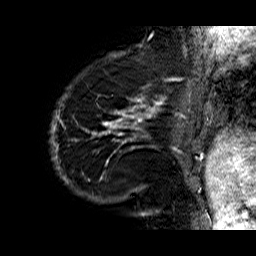
Breast MRI (dynamic contrast-enhanced), one sagittal slice. Slice 7 of 60 in the series (ordered by position). Dynamic contrast-enhanced series, time point 2 of 6 at this slice position (early post-contrast). 1.5 T. TE 6.3 ms, TR 32.9 ms. 4 mm slice thickness. 256 × 256 image matrix, field of view 200 × 200 mm. Female patient. From the clinical record (not read from this slice): setting: breast cancer imaged before/during neoadjuvant chemotherapy; receptor status: HR-positive, HER2-negative.
Annotated regions visible in this slice (semi-automatically segmented with operator editing):
- analysis volume of interest (the breast-tissue region the enhancement analysis was run in; not a lesion): box from (x=50, y=74) to (x=176, y=210) px
- tumour enhancement mask (voxels above the 100 % enhancement threshold inside the analysis volume of interest): (x=50, y=78)–(x=174, y=199)